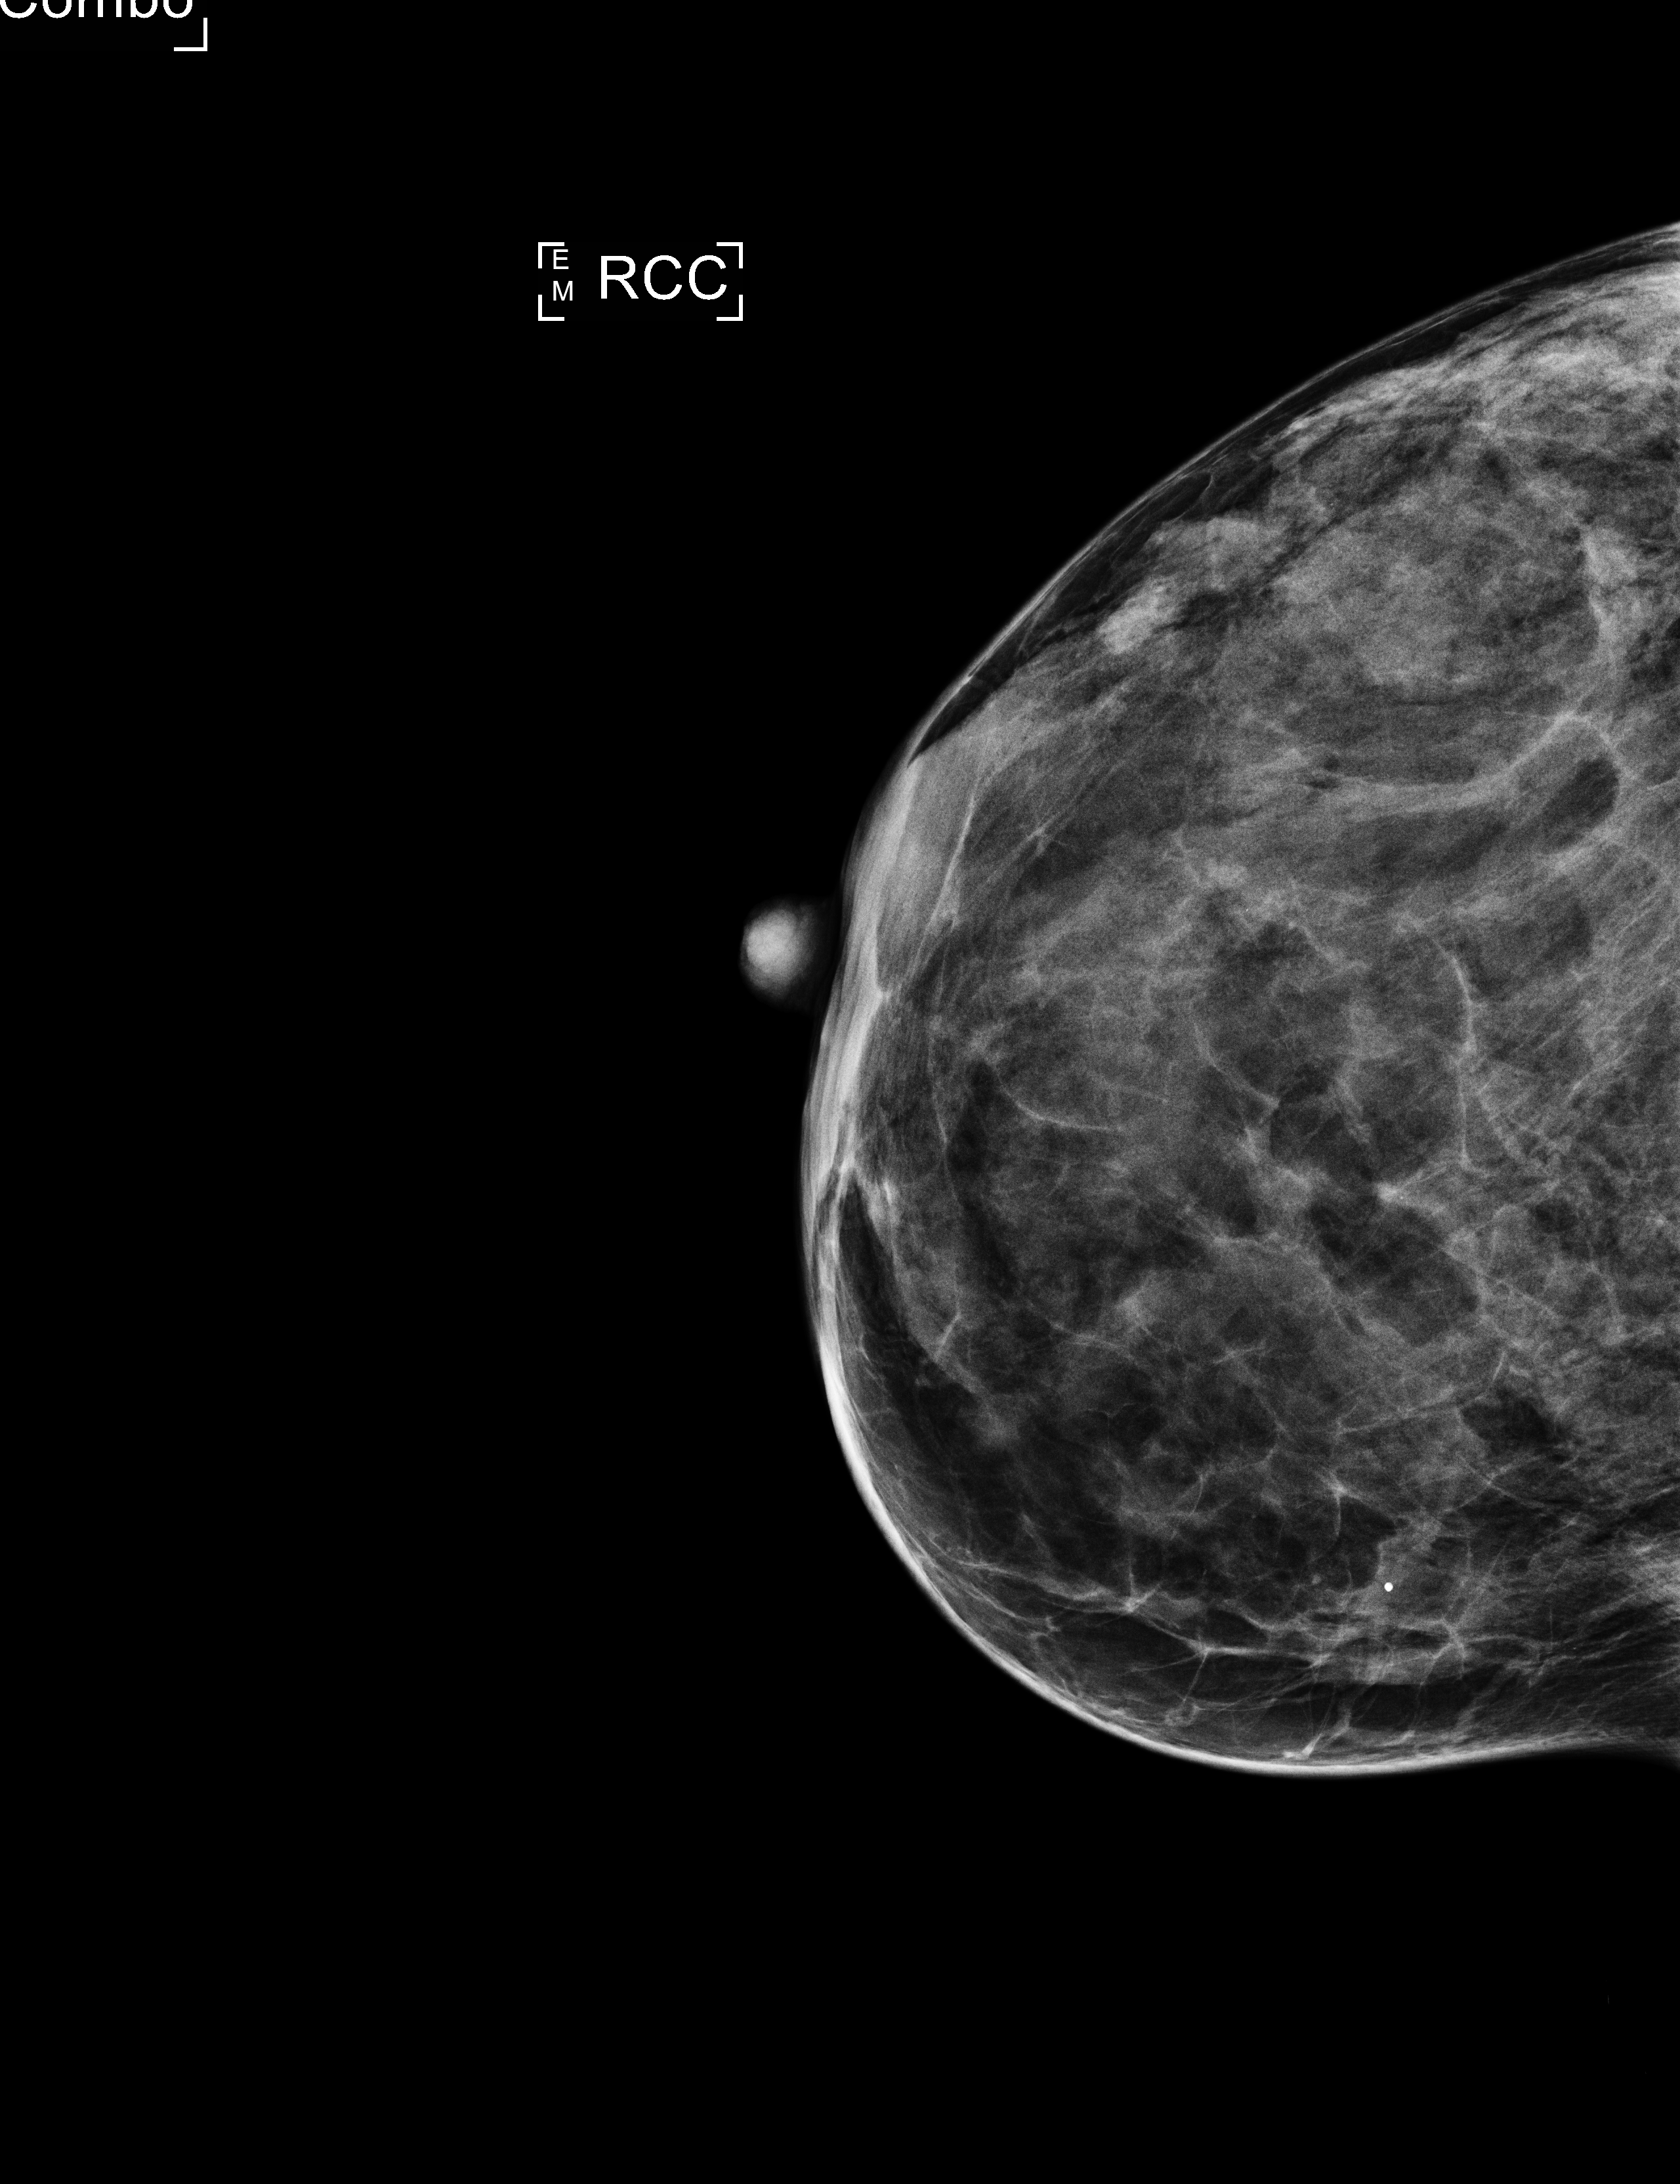
Screening examination; compressed breast thickness 32 mm. Patient: female, 55 years.
Image type: full-field digital mammogram. Breast: right. Projection: CC view.